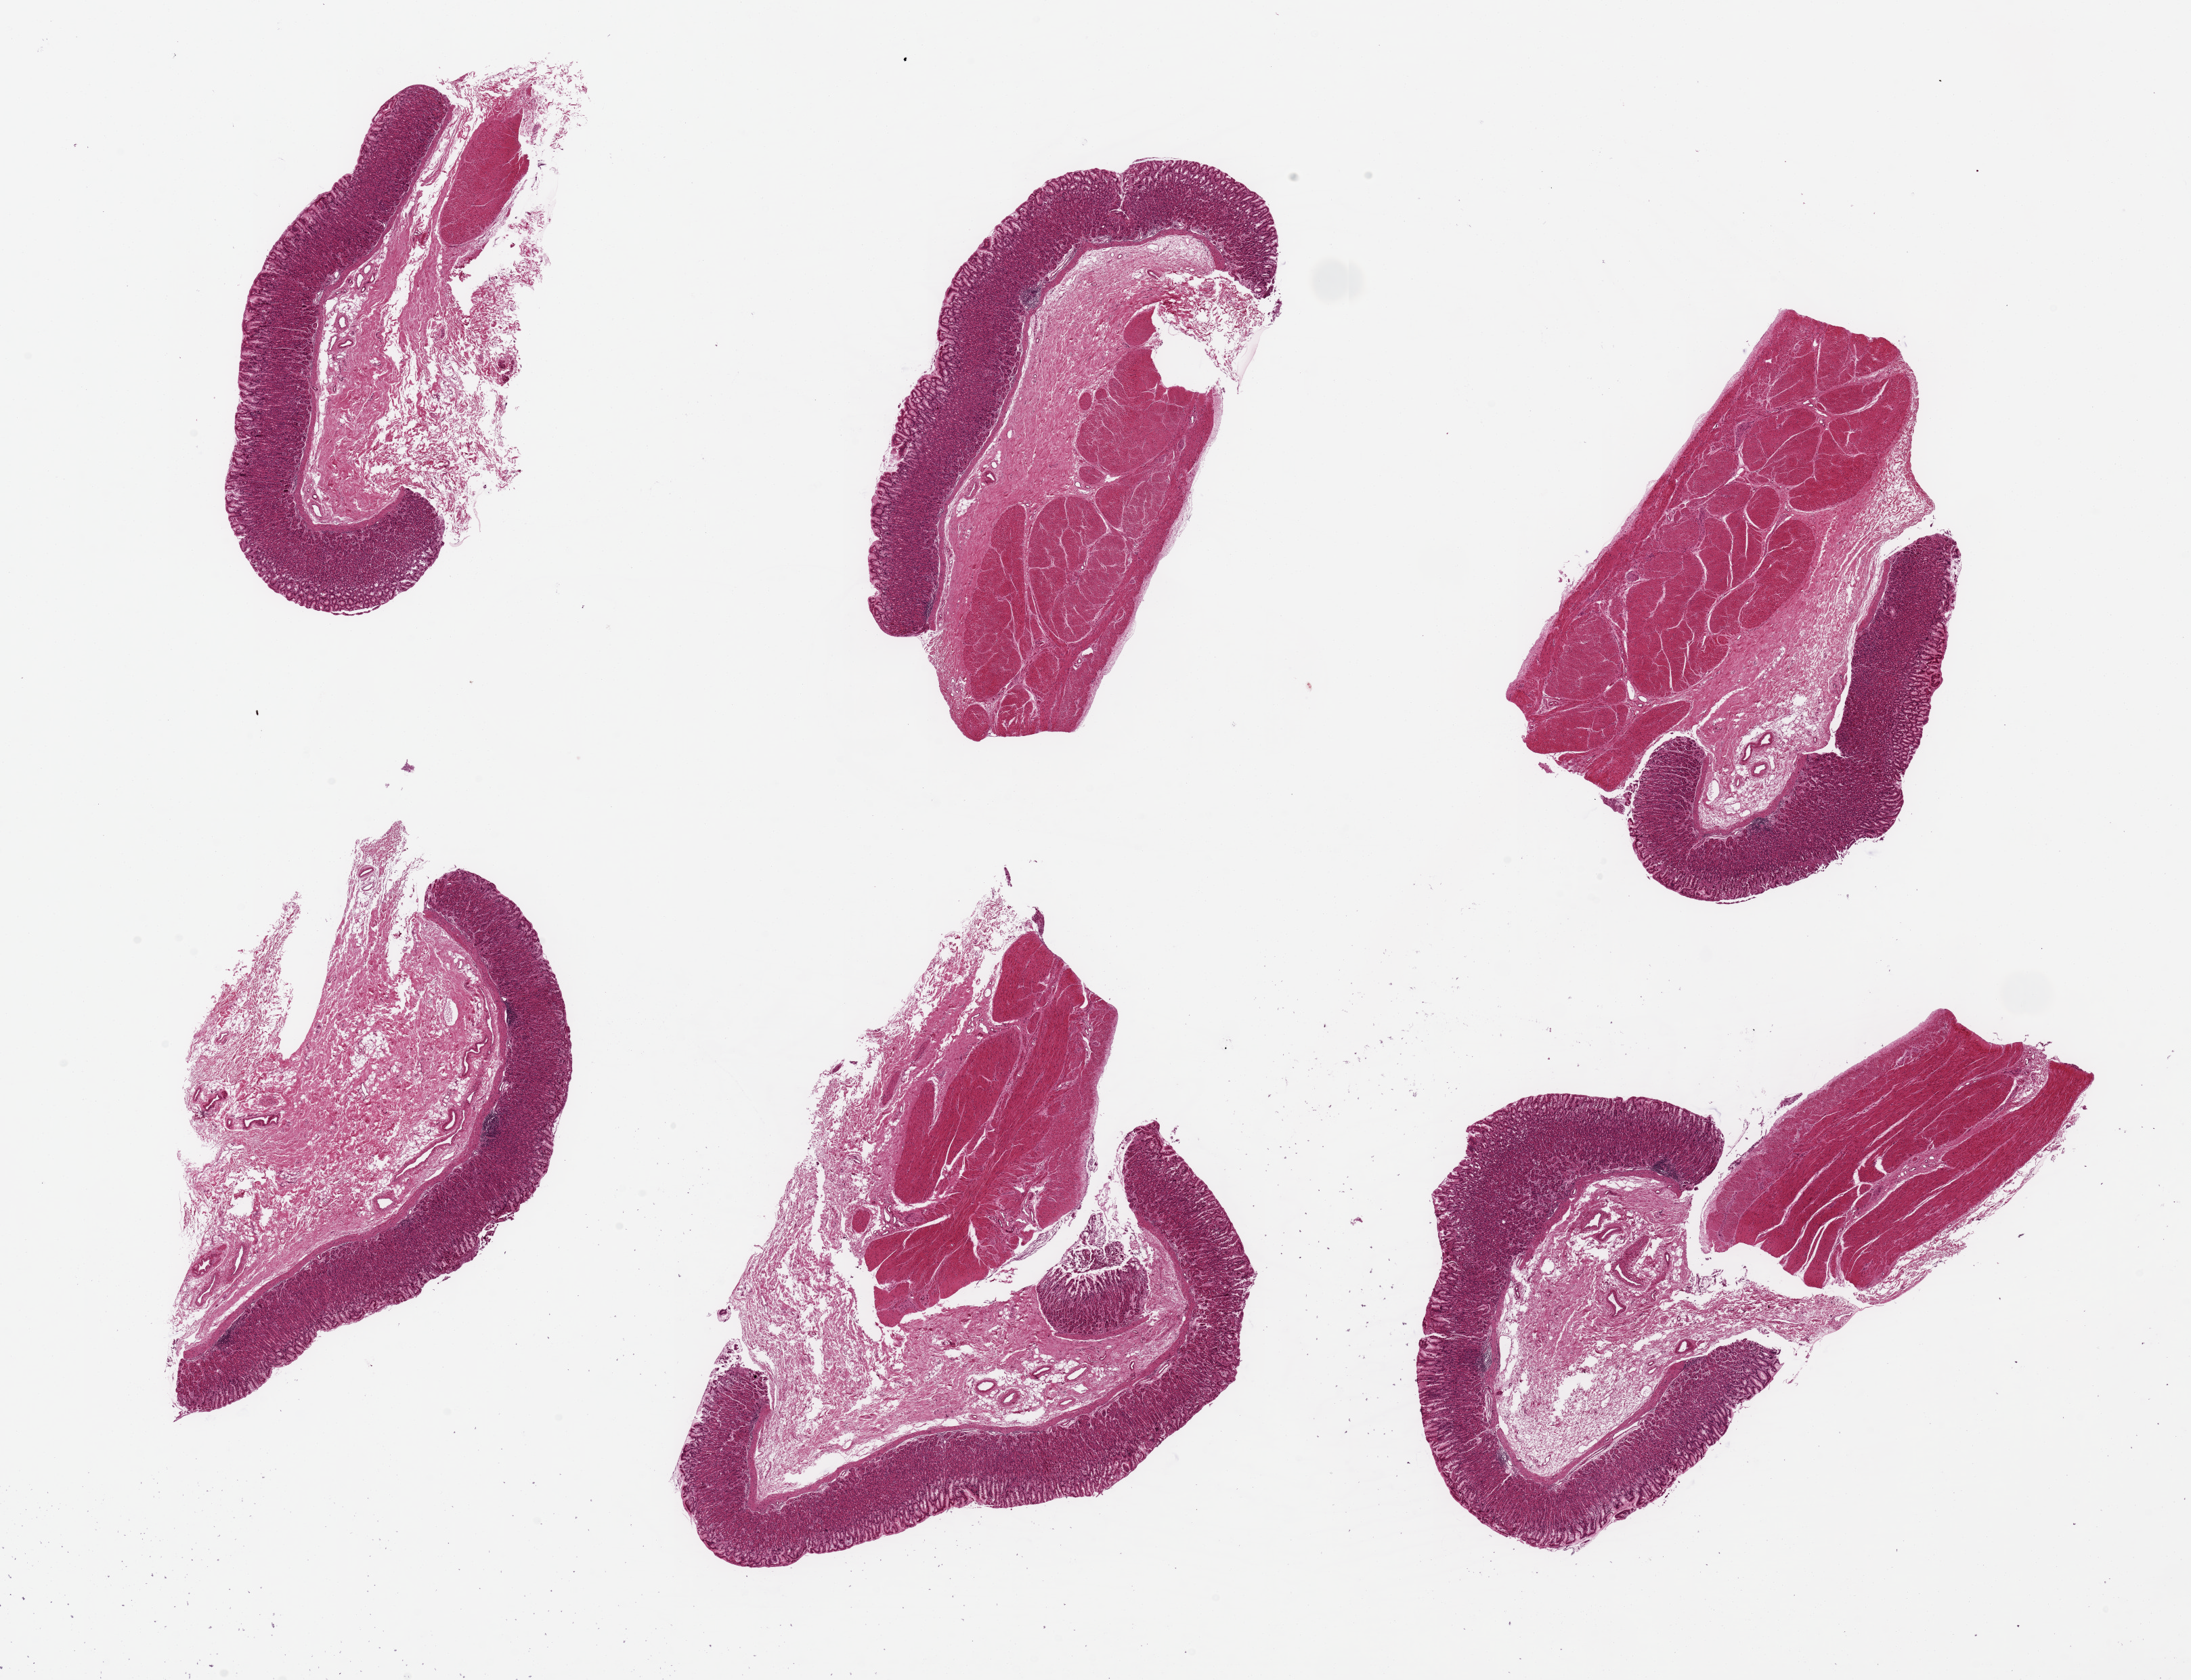
Hematoxylin and eosin (H&E) whole-slide image, brightfield, low-resolution overview of the scanned area, about 25.6 x 19.6 mm (slide scanned at 20x). PAXgene-fixed, paraffin-embedded tissue. Section of stomach (target tissue). Tissue donor sample. Donor: female.
Review note (as recorded): 6 pieces up to 7x3 mm; good mucosal preservation; 4 of 6 have muscularis.